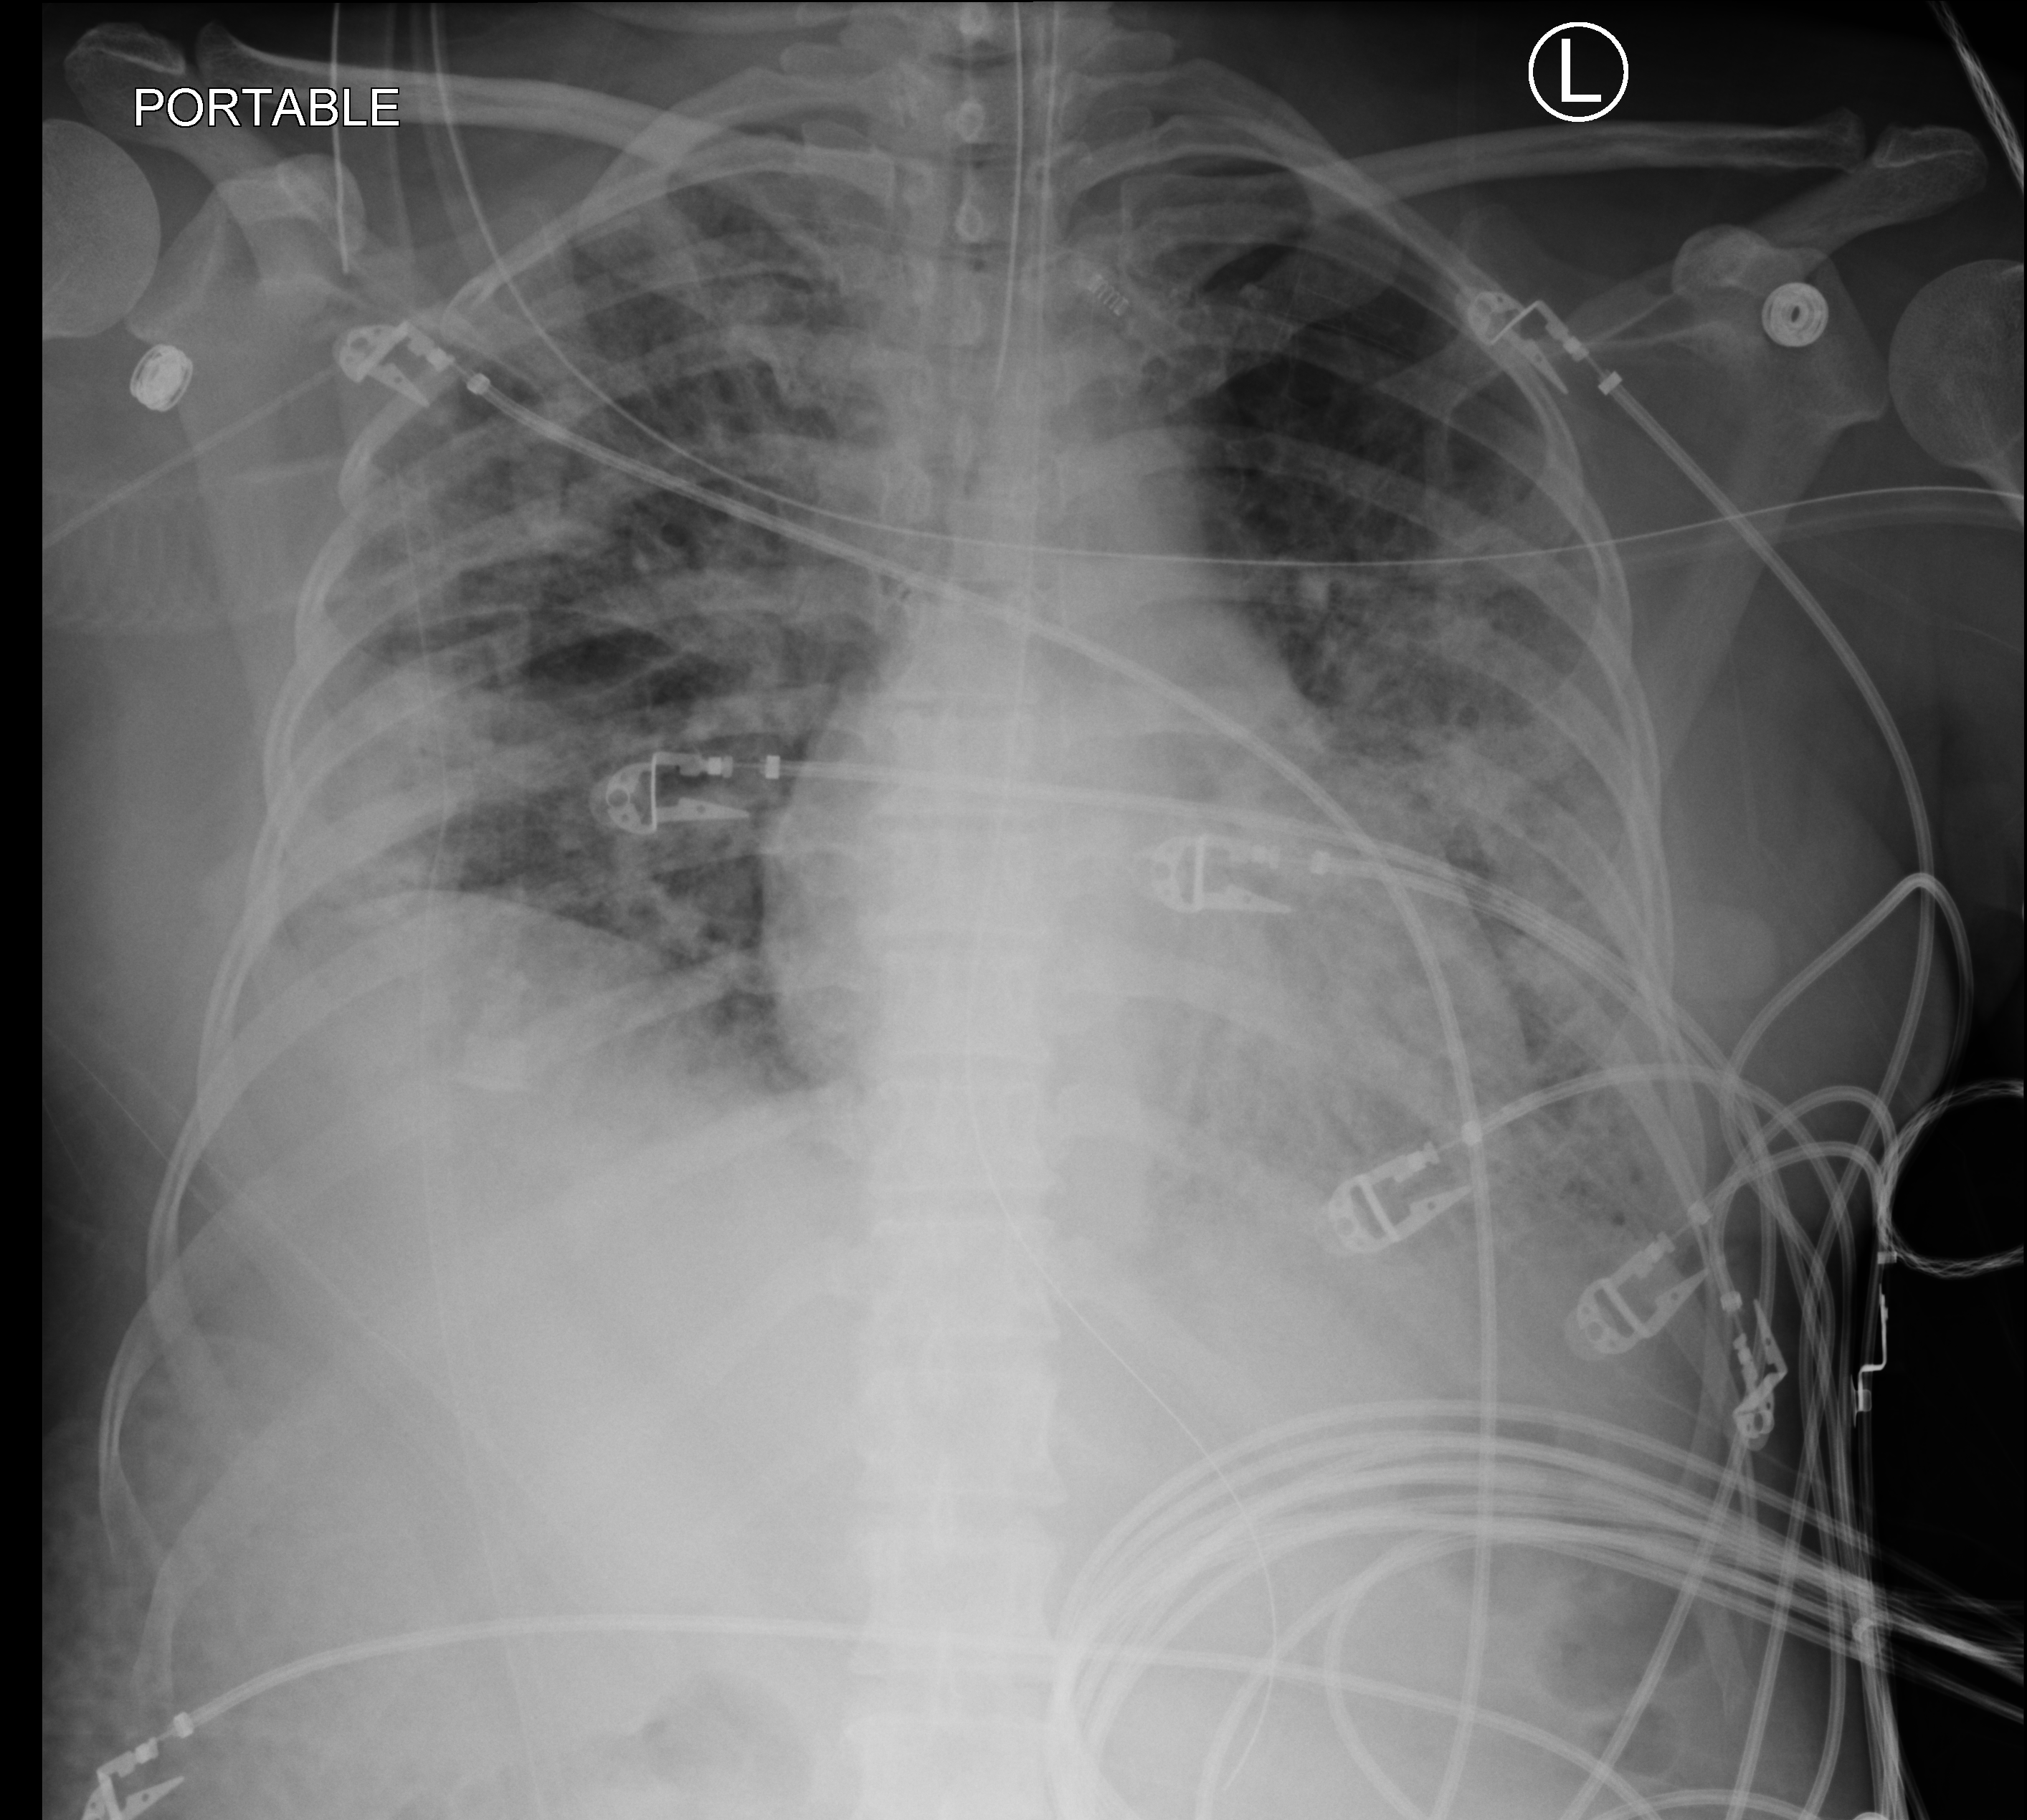
Portable chest radiograph, anteroposterior (AP) projection. Female patient hospitalised with COVID-19, age 18–59 years.
From the hospital-stay record, not from the radiograph (when in the stay this image was taken is not recorded):
- admitted to intensive care during this hospital stay: yes
- mechanically ventilated during this hospital stay: yes